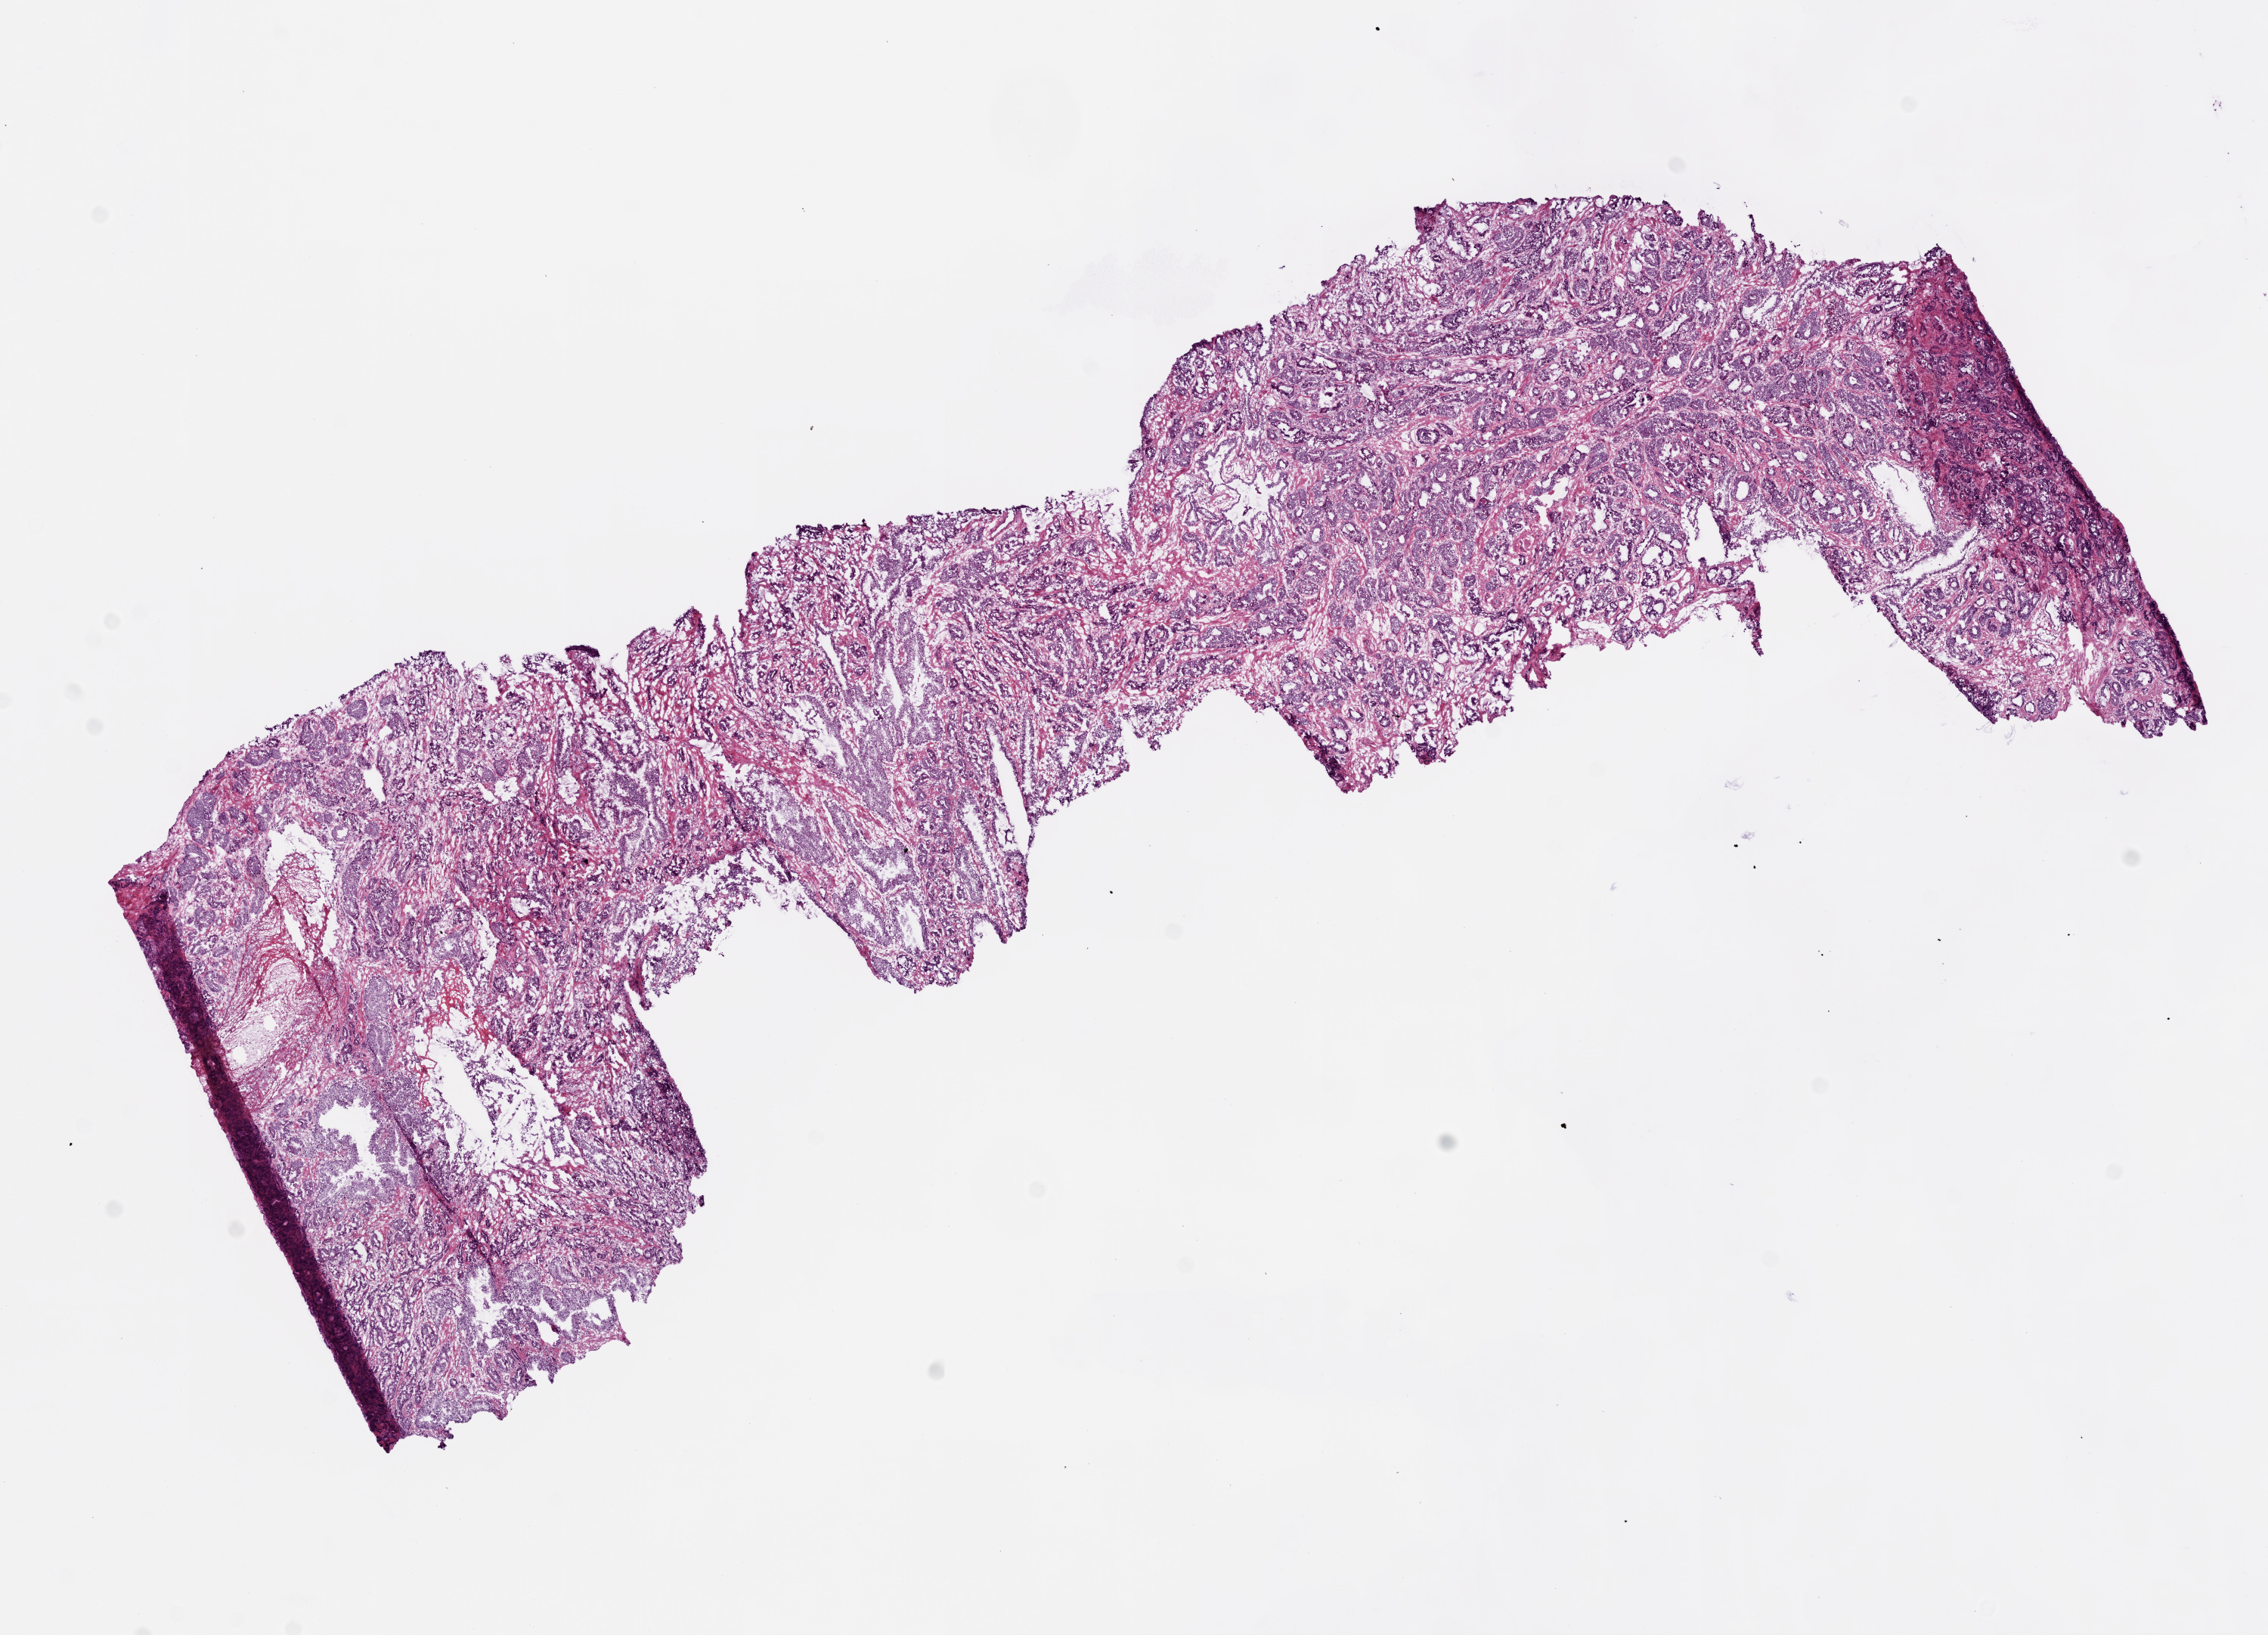
Digitized Hematoxylin and eosin (H&E) stained tissue section (whole slide), low-resolution overview of the scanned area, about 12.0 x 8.7 mm (slide scanned at 20x); frozen section from the top of the tissue portion; prostate, primary tumour sample. Male patient; age at initial diagnosis 55 years. Gleason score: 7 (3+4). Composition of this section per pathologist review: tumour cells 60%, tumour nuclei 75%, normal cells 18%, stromal cells 20%, necrosis 2%. Inflammatory infiltration, as recorded: lymphocyte infiltration 2%, monocyte infiltration 2%, neutrophil infiltration 0%.
Diagnosis: Acinar cell carcinoma (prostate gland). Laterality: bilateral. Lymph nodes positive (case pathology): 0 of 7 examined.